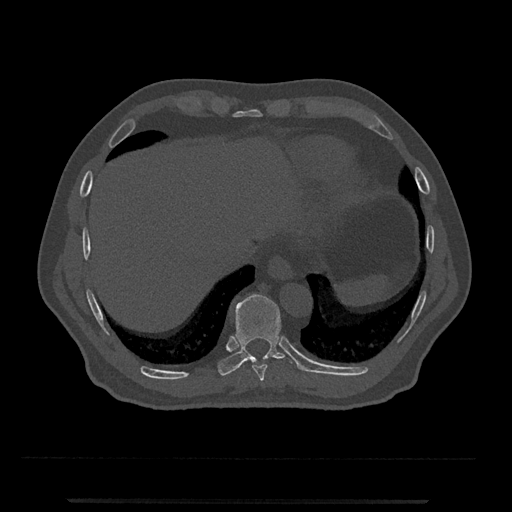
CT including the spine, one axial slice; position 538 of 797 along the scan axis; reconstruction kernel Br40s/3; 120 kVp; bone window (W 1800 / L 400 HU); 0.5 mm slice thickness; 512 × 512 image matrix, field of view 419 × 419 mm. Male patient, age 63 years. Case-level facts recorded for this patient, not image findings: primary cancer: prostate.
Annotated regions visible in this slice (semi-automatically segmented with operator editing):
- T10 vertebra: bounding box [x1, y1, x2, y2] px = [218, 294, 293, 376]
- T9 vertebra: [252, 364, 267, 381]